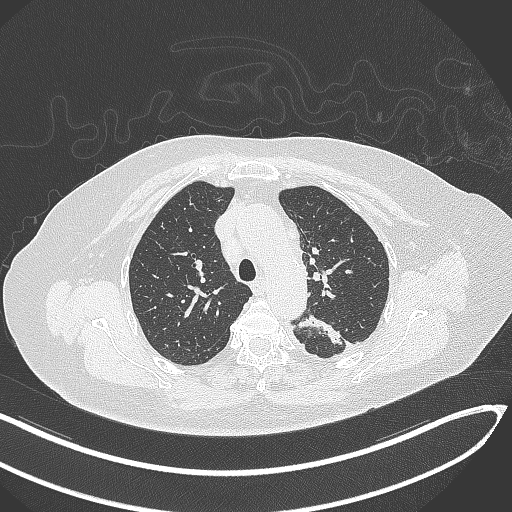
Chest CT, one axial slice; reconstruction kernel B70f; lung window (W 1500 / L -600 HU); 1 mm slice thickness; 512 × 512 image matrix, field of view 400 × 400 mm. Patient: female, 76 years. From the clinical record (not read from this slice): clinical TNM (as recorded): T1c N0 M0.
Annotated regions visible in this slice (rectangle marked by the reading radiologist):
- lung tumour (recorded histology: adenocarcinoma): bounding box [x1, y1, x2, y2] px = [291, 310, 344, 347]